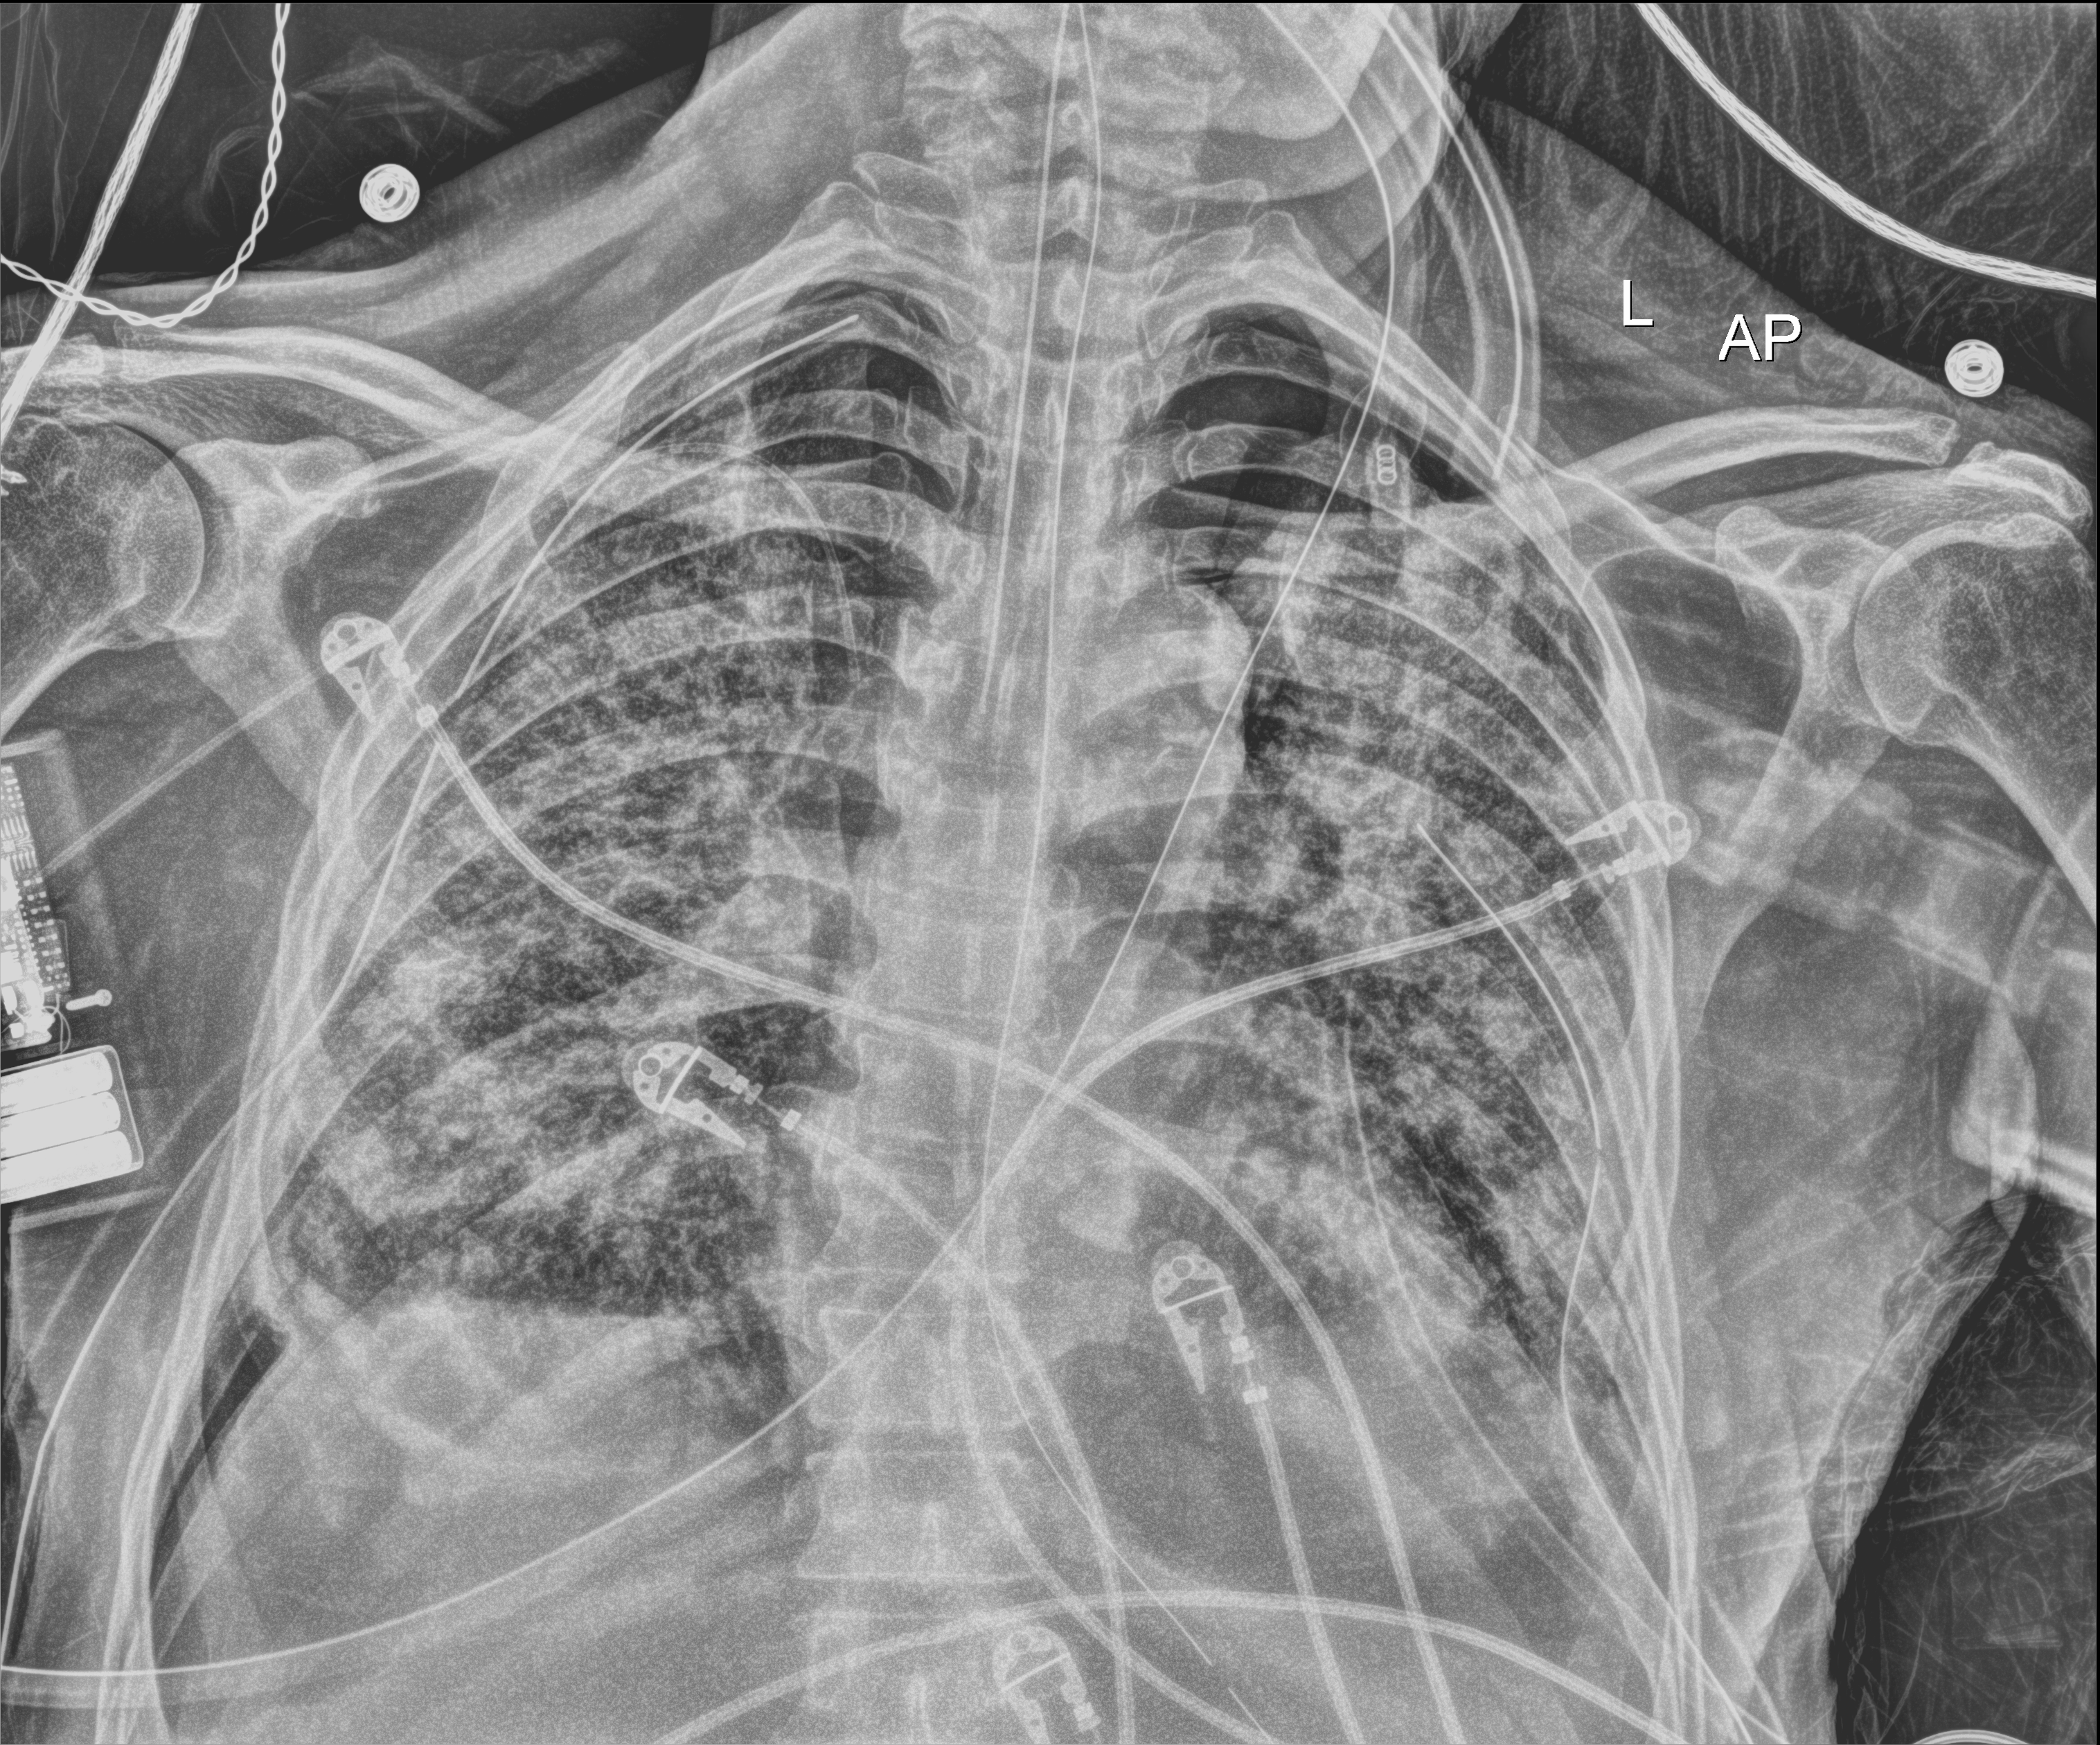
Bedside chest radiograph (digital radiography); anteroposterior (AP) projection. Patient hospitalised with COVID-19; male, aged 60–74 years.
From the hospital-stay record, not from the radiograph (when in the stay this image was taken is not recorded):
- other chronic lung disease (admission record): yes
- length of hospital stay: 65 days
- admitted to intensive care during this hospital stay: yes